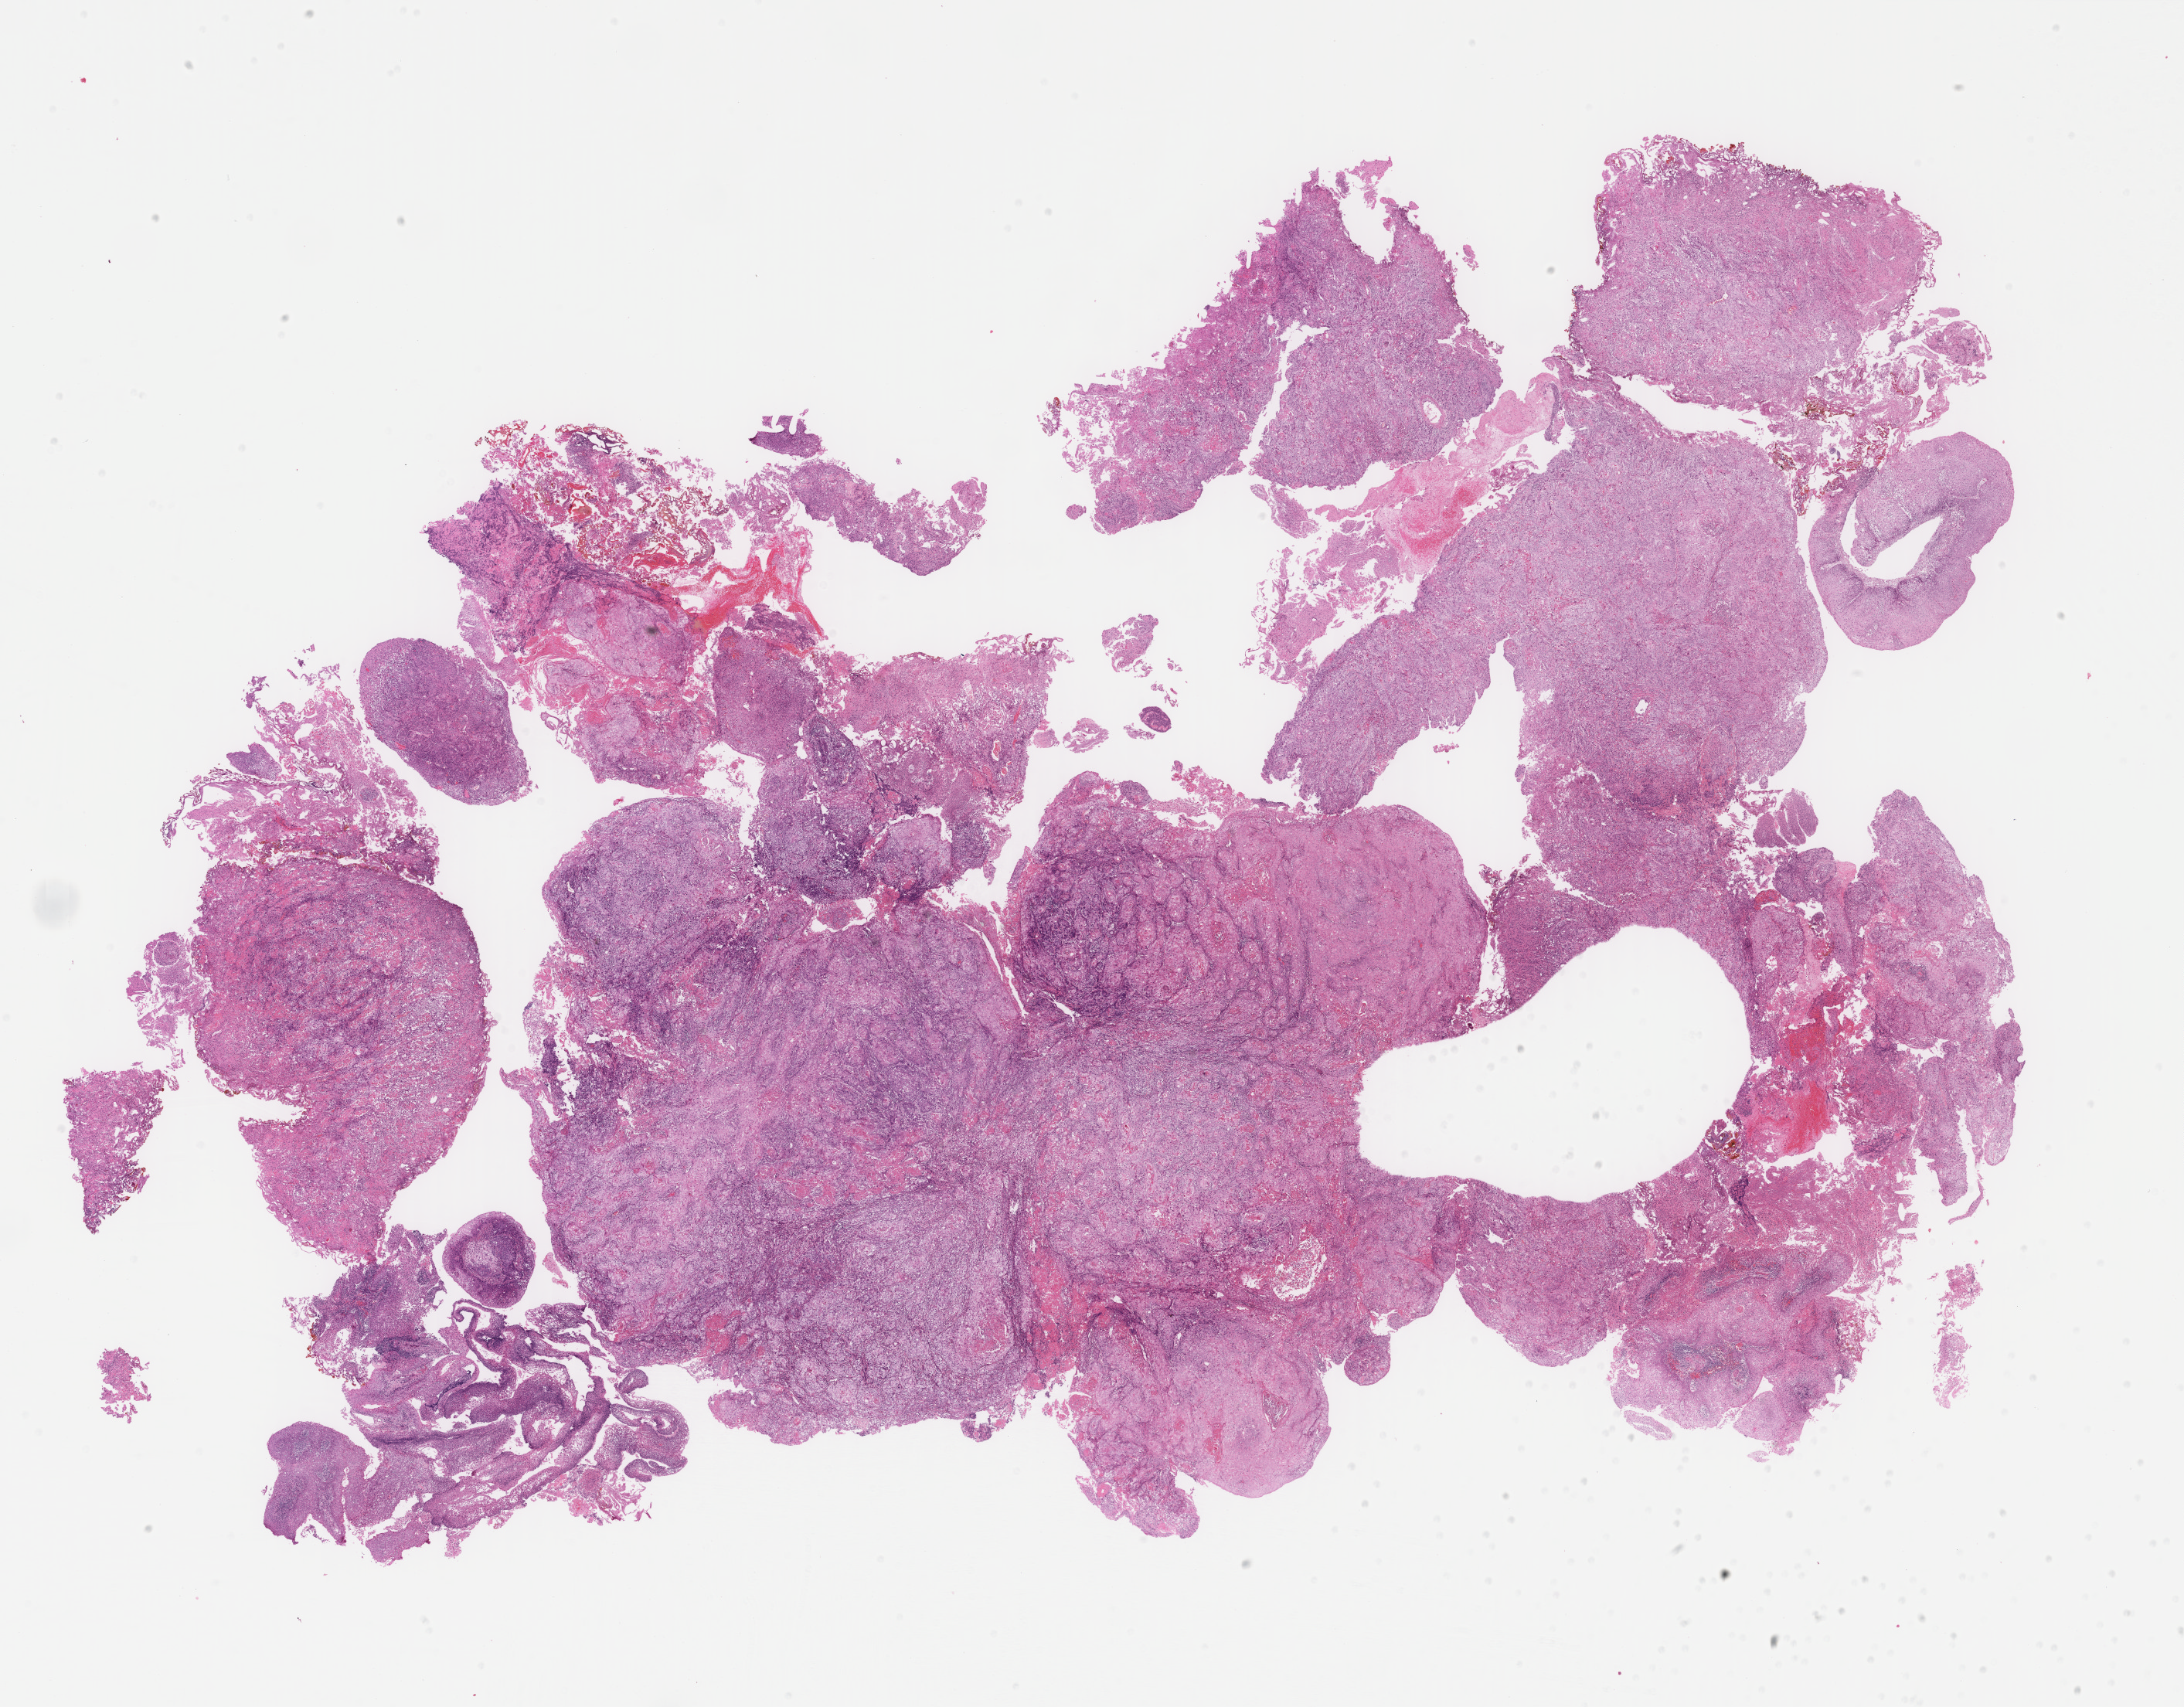
Whole-slide histology image, H&E — a low-resolution overview of the entire scanned area, about 22.4 x 17.5 mm (from a 40x scan), FFPE section, primary tumour sample from the bladder. Female patient; age at initial diagnosis 56 years.
Pathologic diagnosis: Transitional cell carcinoma.